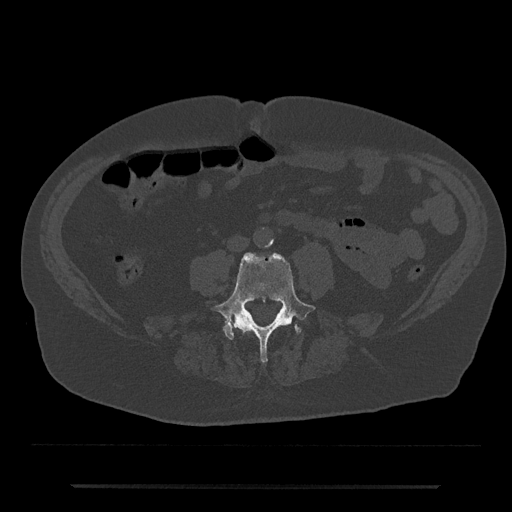
CT including the spine, one axial slice; position 352 of 797 along the scan axis; reconstruction kernel Br40s/3; bone window (W 1800 / L 400 HU); 0.5 mm slice thickness; 512 × 512 image matrix, field of view 434 × 434 mm. Patient: male, 80 years. From the clinical record (not read from this slice): primary cancer: prostate; vertebrae with lytic lesions (as recorded): L1, T11.
Structures marked on this image (semi-automatic segmentation, software-assisted and operator-edited):
- L4 vertebra: bounding box <211,252,316,363> (left, top, right, bottom; pixels)